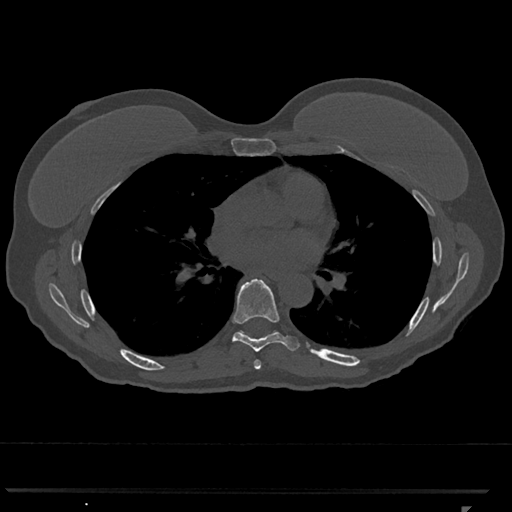
CT including the spine, one axial slice; position 709 of 793 along the scan axis; reconstruction kernel Br40s/3; 120 kVp; bone window (W 1800 / L 400 HU); 0.5 mm slice thickness; 512 × 512 image matrix. Patient: female, 62 years. Case-level facts recorded for this patient, not image findings: primary cancer: renal.
Structures marked on this image (semi-automatic segmentation, software-assisted and operator-edited):
- T6 vertebra: bounding box (x1, y1, x2, y2) in pixels: (254, 360, 262, 370)
- T7 vertebra: (224, 279, 299, 352)